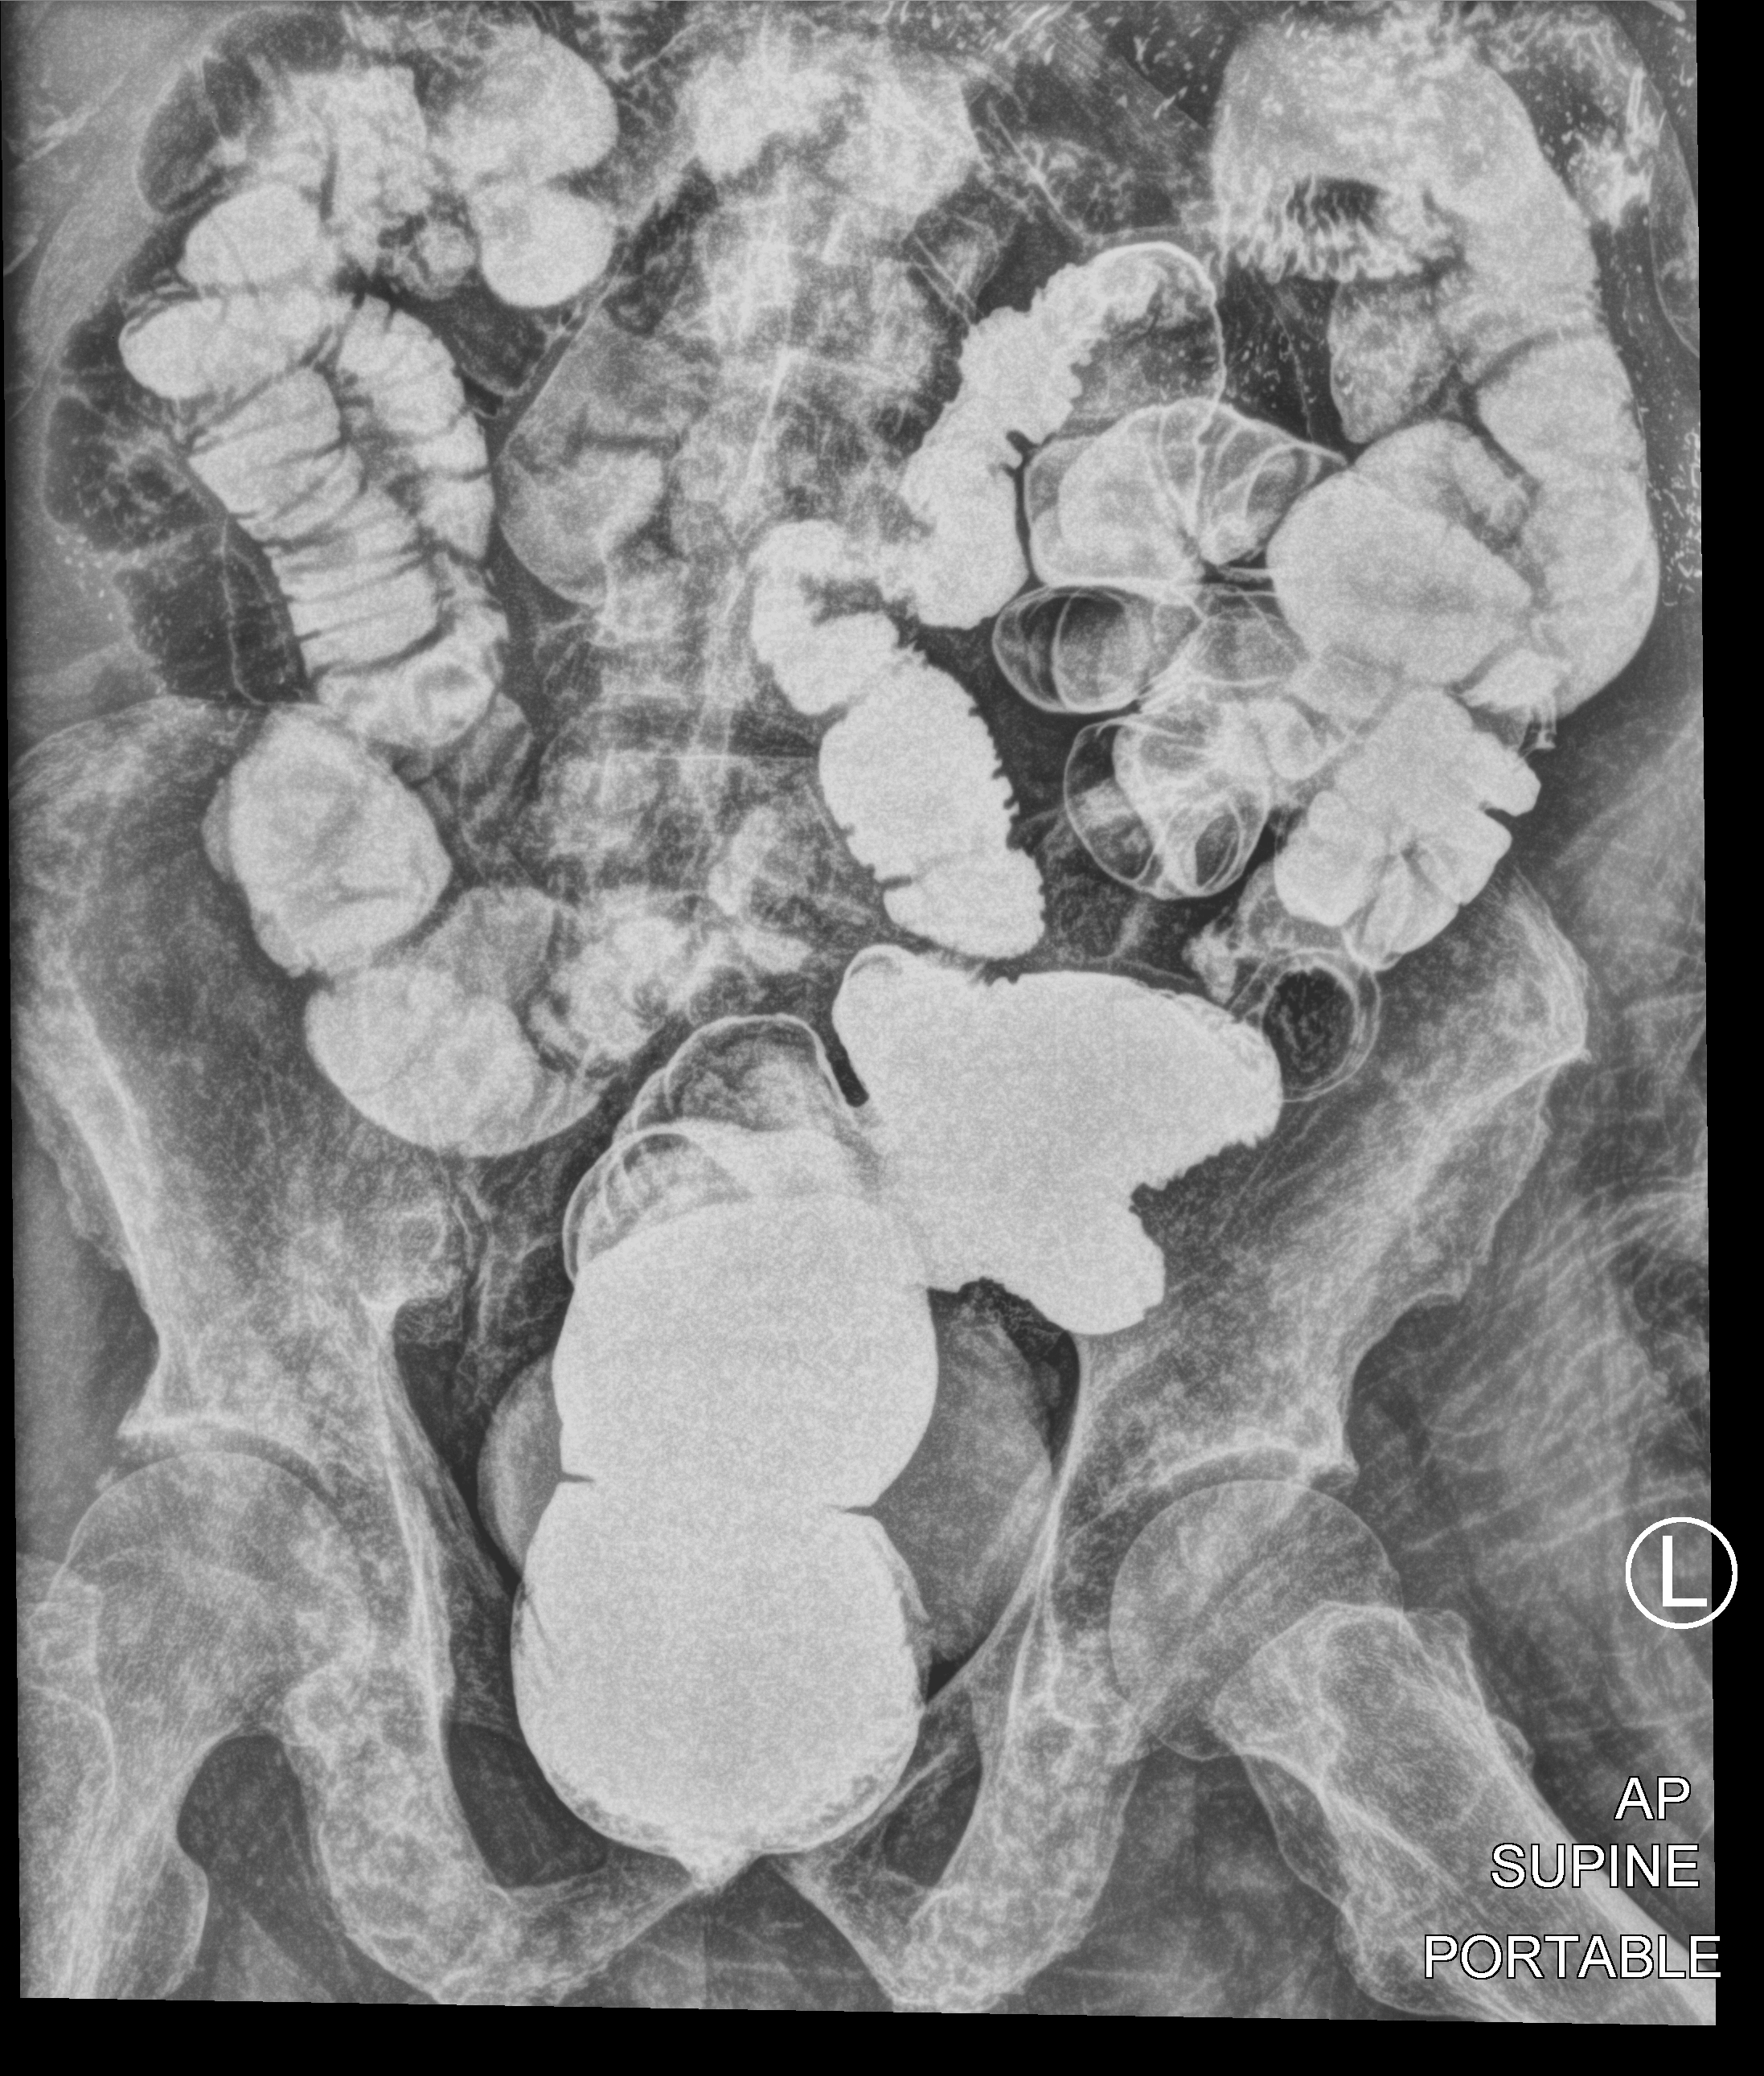
Bedside abdomen radiograph (computed radiography). Male patient hospitalised with COVID-19, age 75–90 years.
From the hospital-stay record, not from the radiograph (when in the stay this image was taken is not recorded): mechanically ventilated during this hospital stay: no.